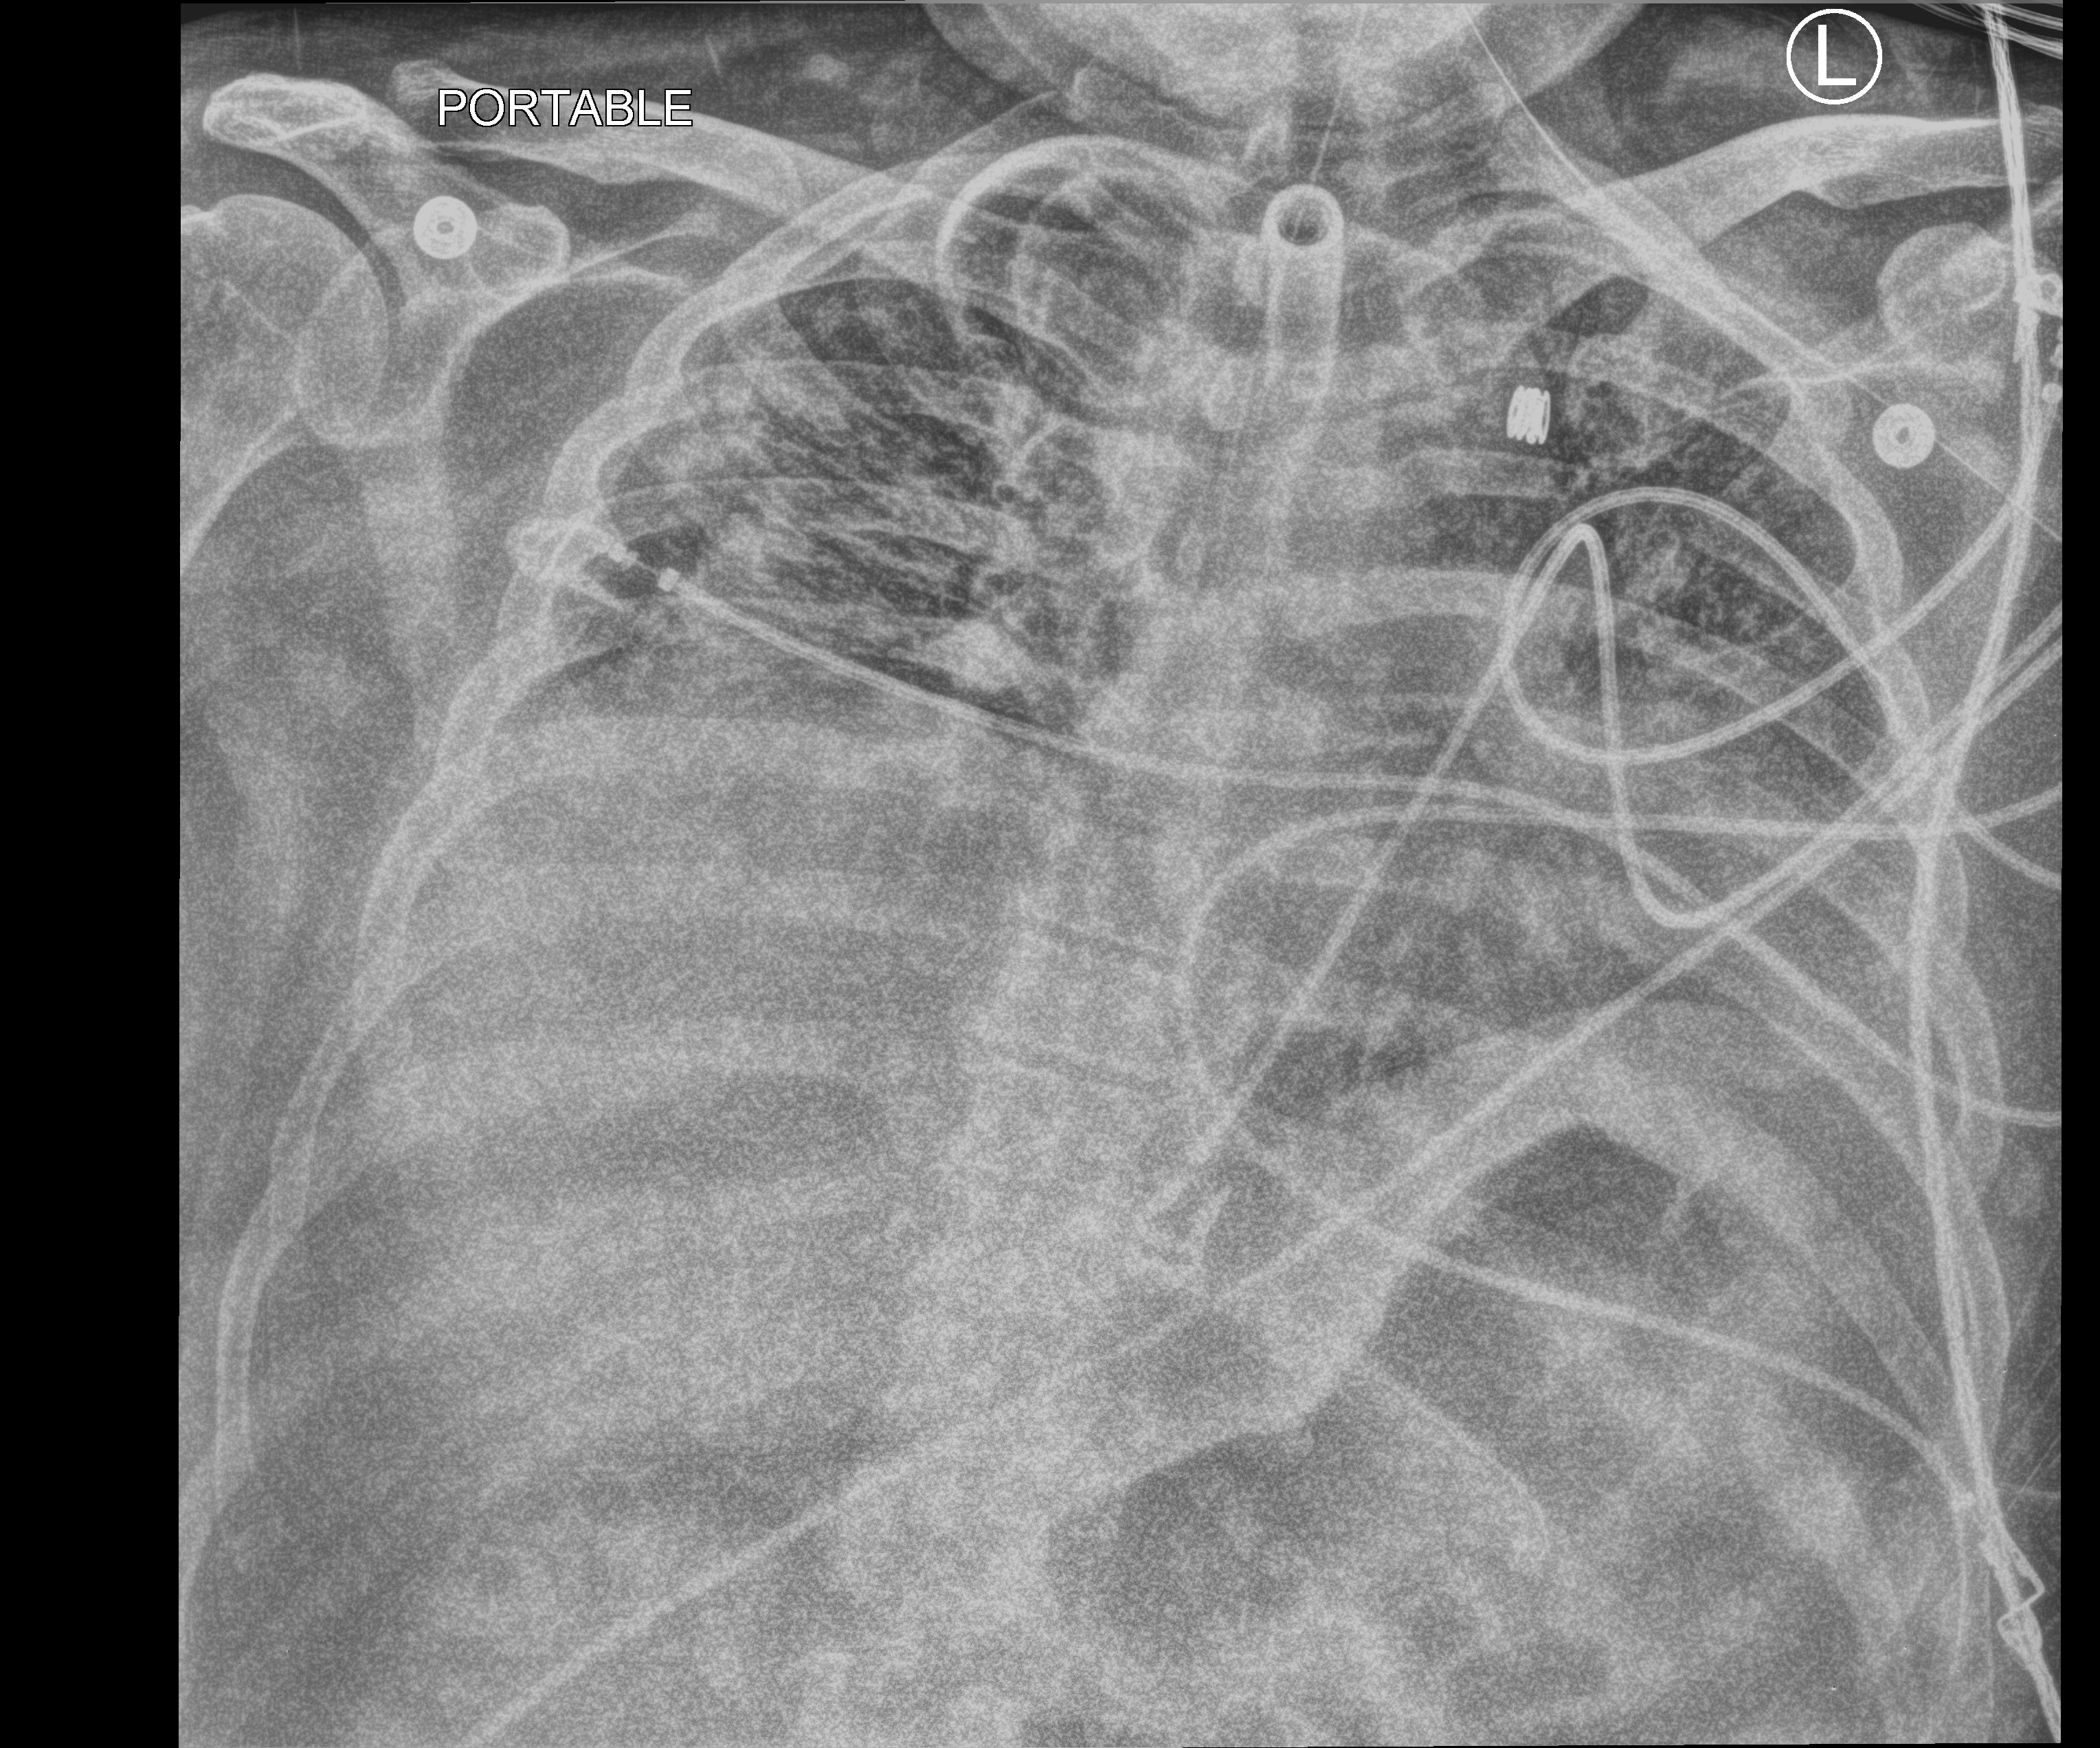
Chest X-ray (portable). Patient hospitalised with COVID-19; male, aged 18–59 years.
Admission-level facts for this patient (not findings on this image; timing relative to this image not recorded):
- COPD (admission record): no